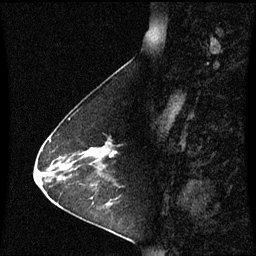
Breast MRI (dynamic contrast-enhanced), one sagittal slice; slice 22 of 60 in the series (ordered by position); dynamic contrast-enhanced series, image 2 of 3 at this slice position (ordered by acquisition); 1.5 T; TE 4.2 ms, TR 8.9 ms; 2 mm slice thickness; 256 × 256 image matrix. Female patient, age 63 years. From the clinical record (not read from this slice): setting: breast cancer imaged before/during neoadjuvant chemotherapy; receptor status: HR-positive, HER2-negative.
Structures marked on this image (semi-automatic segmentation, software-assisted and operator-edited):
- analysis volume of interest (the breast-tissue region the enhancement analysis was run in; not a lesion): bounding box (x1, y1, x2, y2) in pixels: (76, 139, 117, 178)
- tumour enhancement mask (voxels above the 70 % enhancement threshold inside the analysis volume of interest): (110, 151, 117, 158)